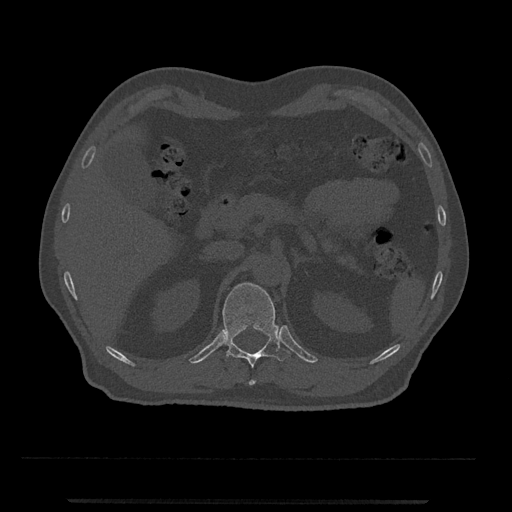
CT including the spine, one axial slice; position 402 of 797 along the scan axis; reconstruction kernel Br40s/3; bone window (W 1800 / L 400 HU); 512 × 512 image matrix, field of view 419 × 419 mm. Male patient, age 63 years. From the clinical record (not read from this slice): primary cancer: prostate.
Structures marked on this image (semi-automatic segmentation, software-assisted and operator-edited):
- T12 vertebra: bounding box [x1, y1, x2, y2] px = [221, 282, 290, 385]